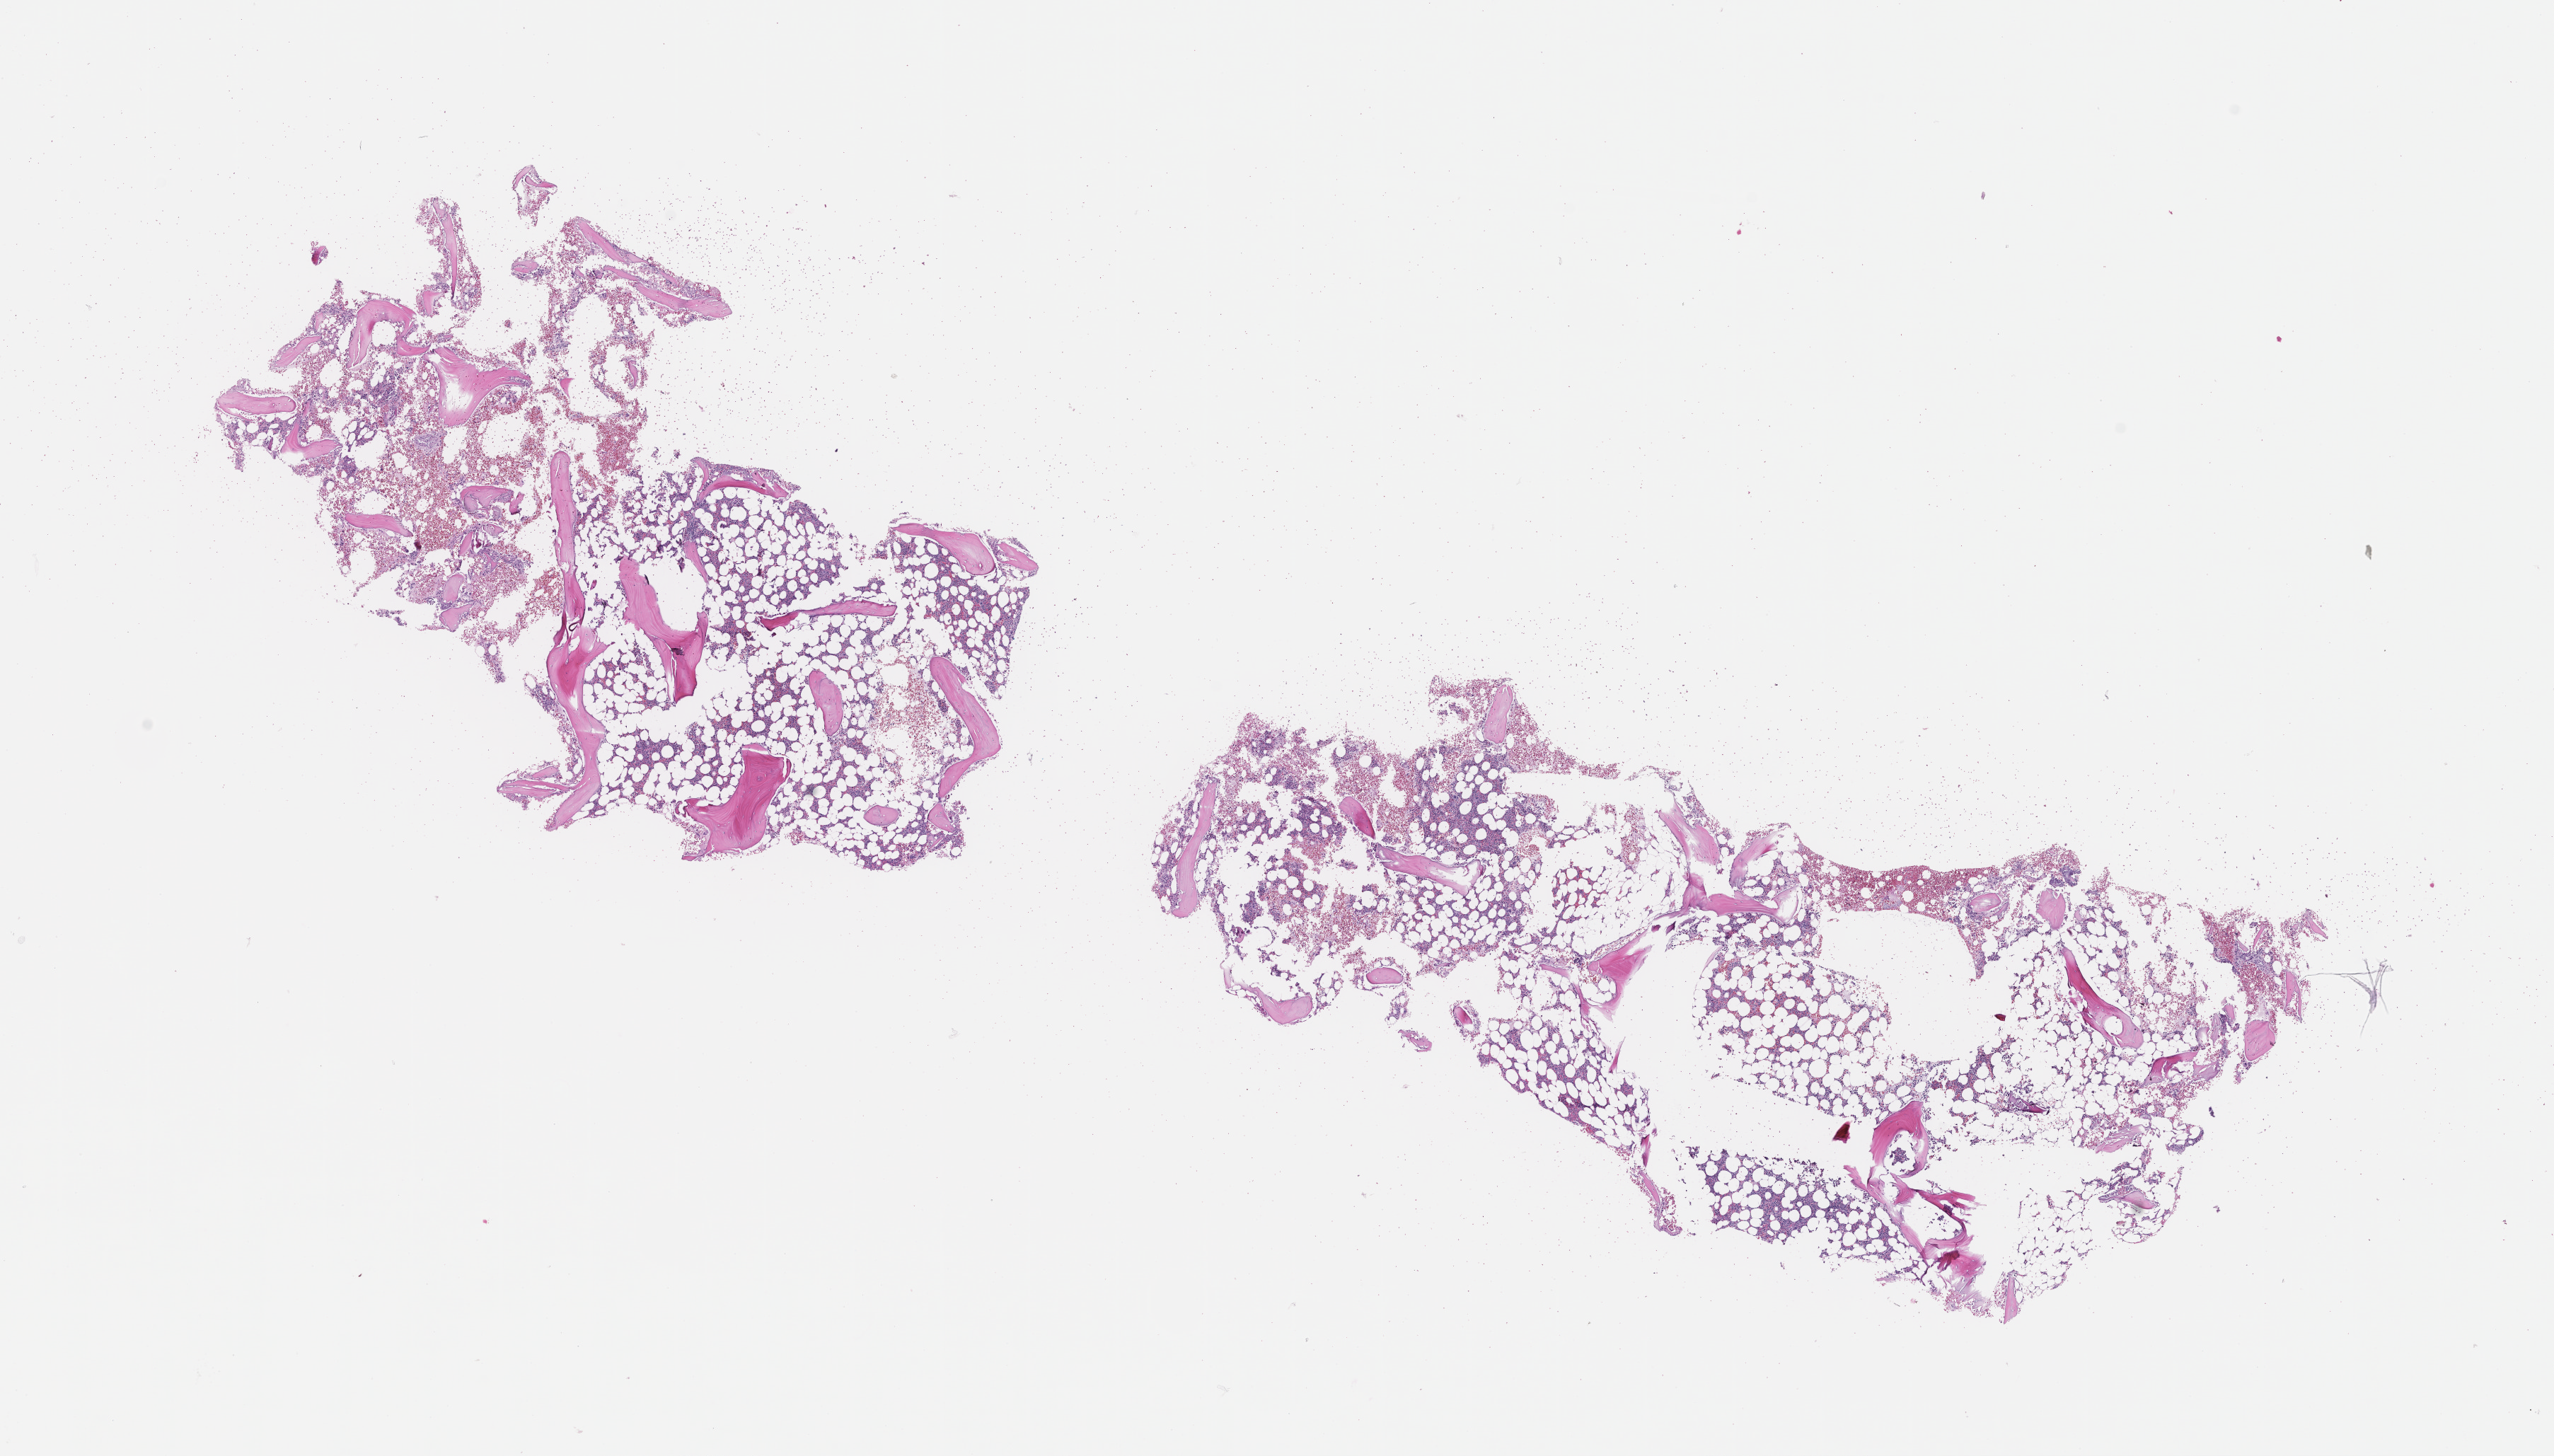
Digitized H&E-stained section, whole scanned area (about 14.6 x 8.3 mm) shown as a low-resolution overview, formalin-fixed paraffin-embedded section, site: bone marrow, archival tissue. Patient sex: female.
• this section: primary tumour tissue
• diagnosis: Acute Myeloid Leukemia Not Otherwise Specified